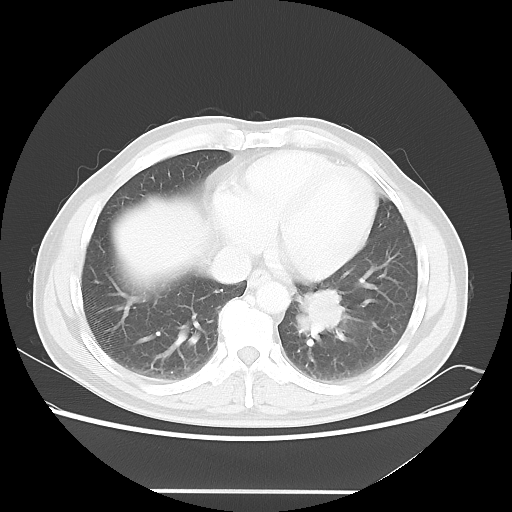
Chest CT, one axial slice. Slice 17 of 53 in the series (ordered by position). Reconstruction kernel LUNG. 120 kVp. Lung window (W 1500 / L -600 HU). 5 mm slice thickness. 512 × 512 image matrix. Patient: male, 61 years. Case-level facts recorded for this patient, not image findings: clinical TNM (as recorded): T1c N0 M0; histopathological grade: G3.
Outlined on this slice (rectangle marked by the reading radiologist):
- lung tumour (recorded histology: adenocarcinoma): bounding box <292,285,351,355> (left, top, right, bottom; pixels)